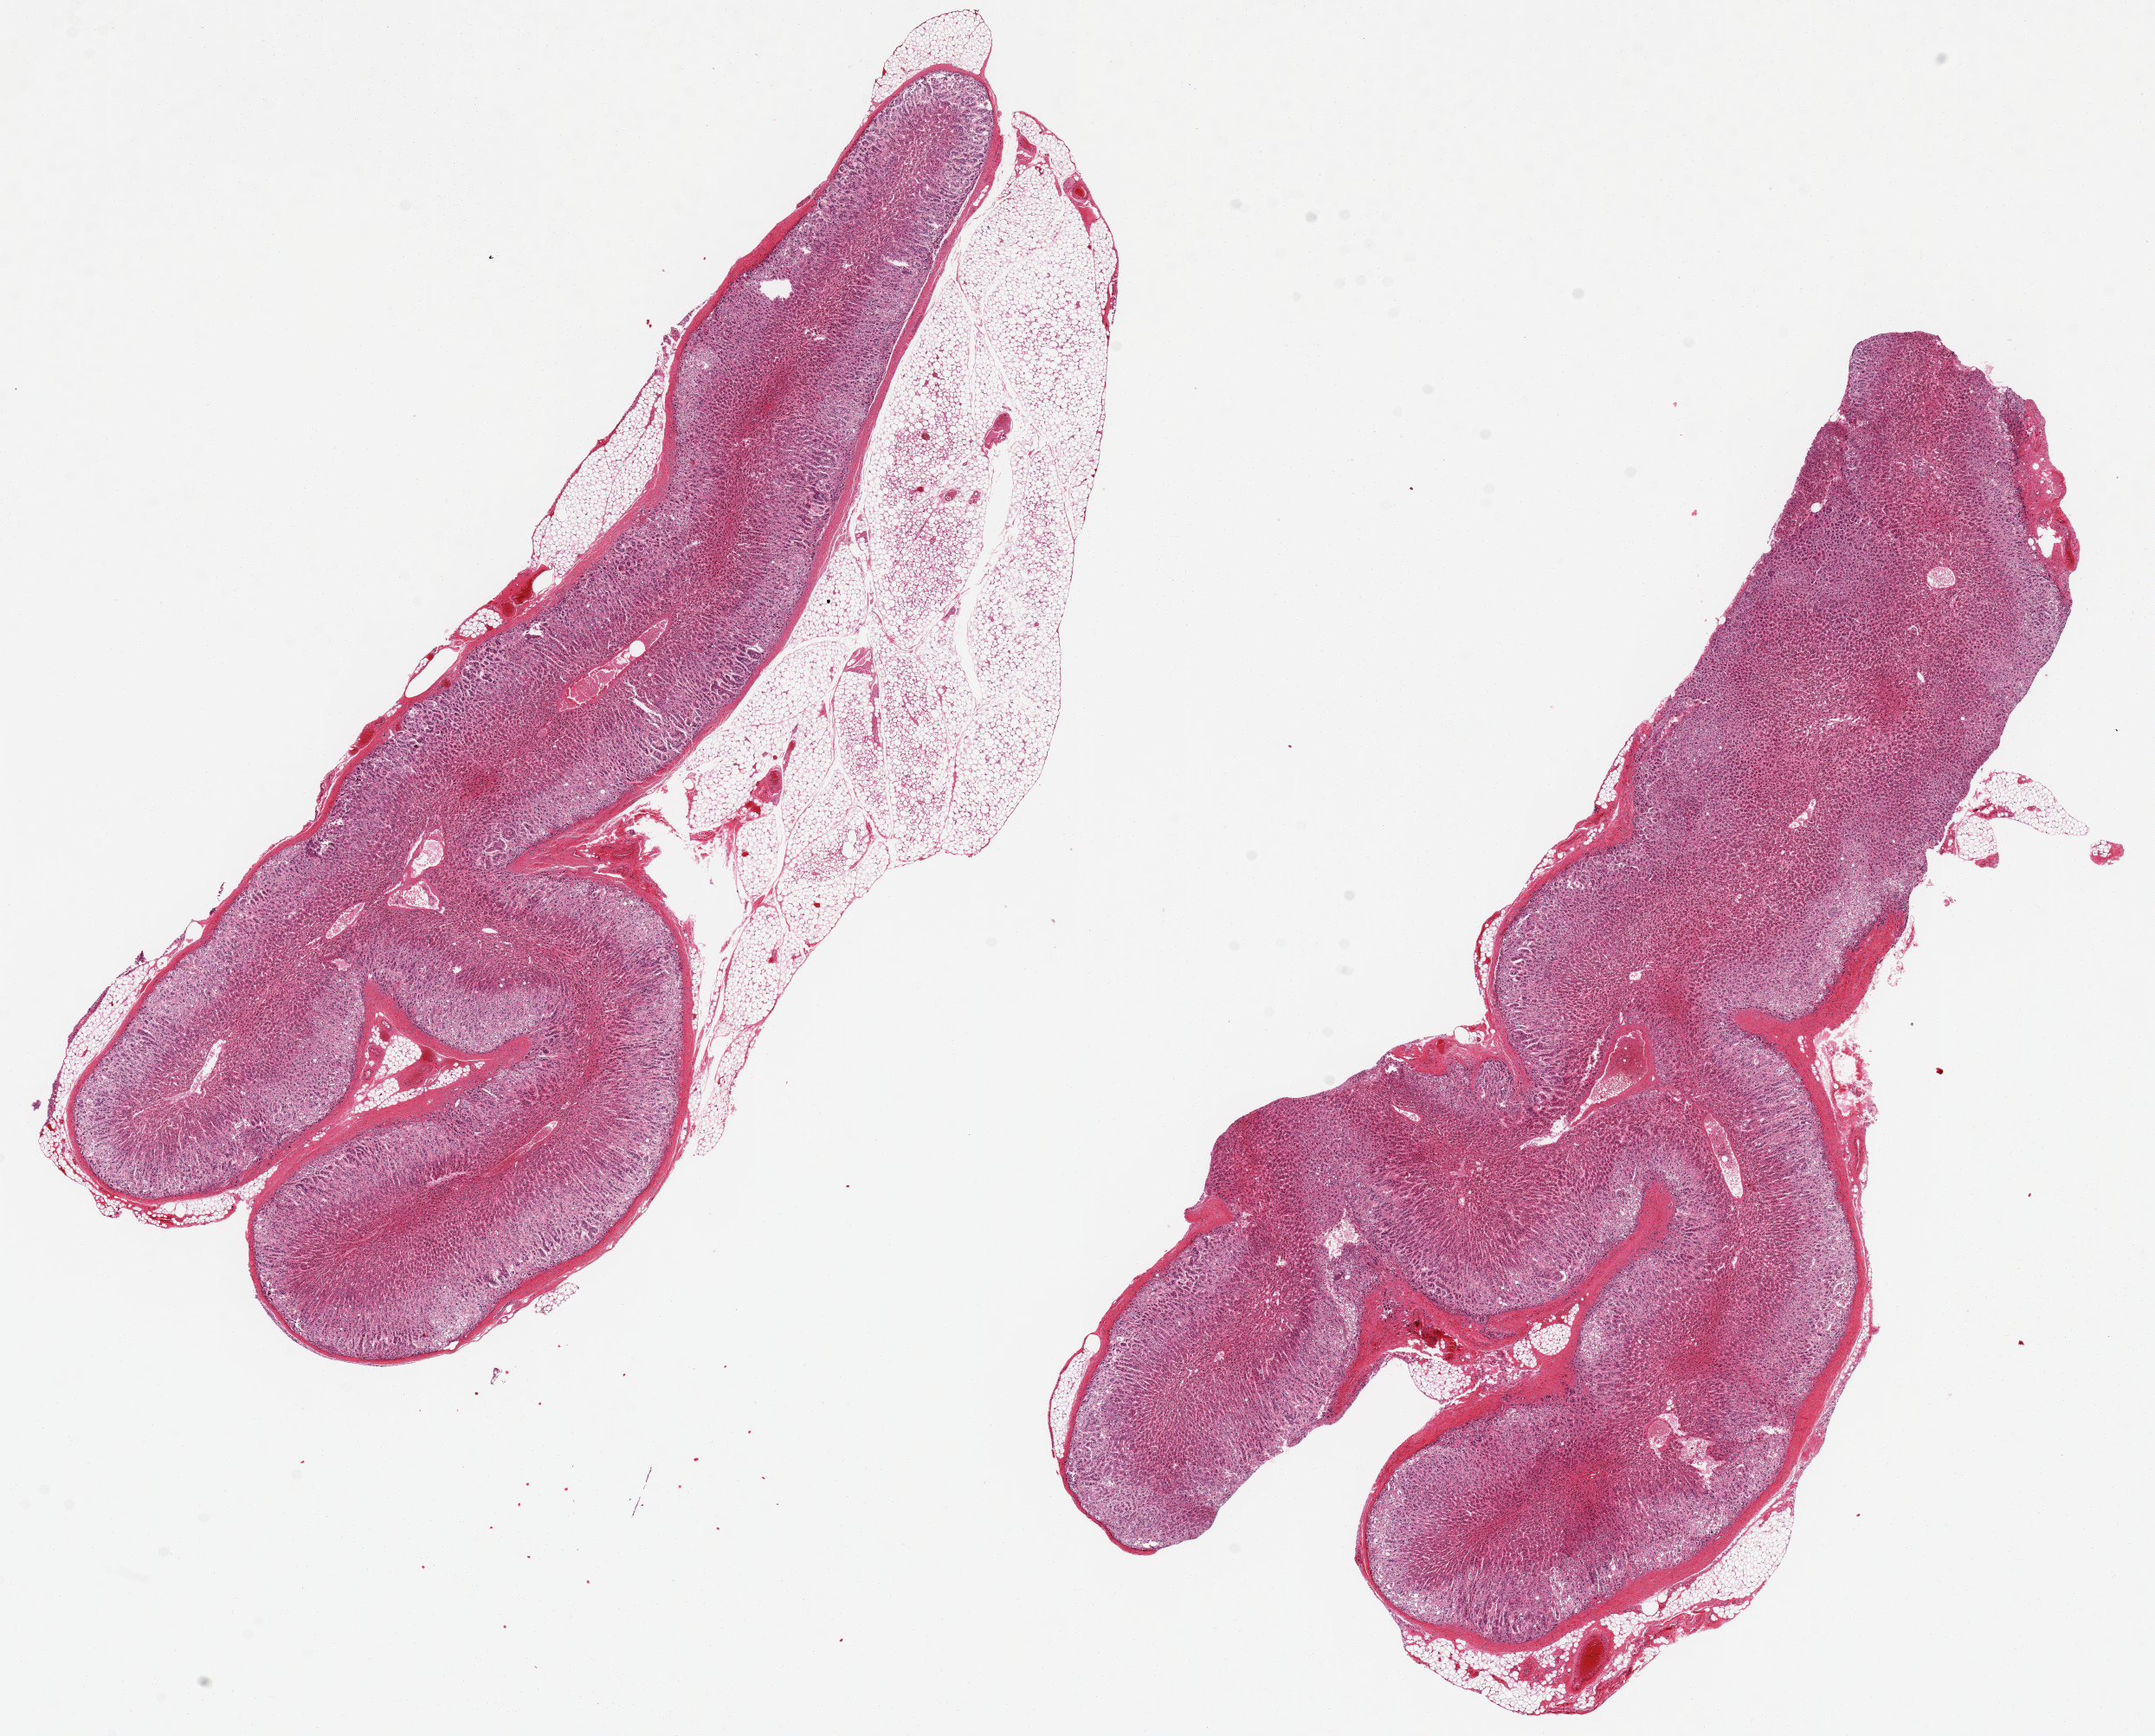
Digitized hematoxylin and eosin (H&E)-stained section — low-resolution overview of the scanned area, about 19.7 x 15.9 mm. PAXgene-fixed paraffin-embedded (PFPE) section. Section of adrenal gland (target tissue). Tissue donor sample. Donor: male.
Reviewer comment on this tissue sample: 2 pieces 13x5 mm each; 1 has 7.5x2 mm adipose tissue along edge.